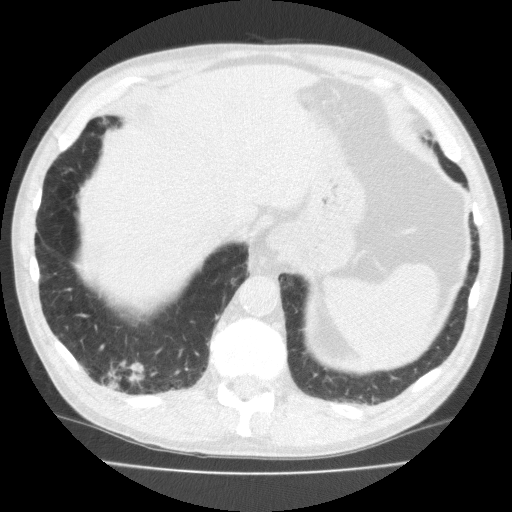
Chest CT (low-dose screening protocol), one axial image; second annual screen; lung window (W 1500 / L -600 HU); 2 mm slice thickness. Male participant, aged 70 years at enrolment. Current smoker at enrolment.
Expert reader's lesion annotation, bounding box (x1, y1, x2, y2) in pixels: (88, 349, 160, 399). Reader record for this screening exam (exam-level; its link to the box is not recorded): non-calcified nodule or mass ≥4 mm, right lower lobe, 18 × 13 mm, spiculated (stellate) margins, soft tissue attenuation, pre-existing on the prior screen: no. Later outcome: lung cancer diagnosed 64 days after this screen — squamous cell carcinoma, NOS, right lower lobe, moderately differentiated (G2), stage IA (AJCC 6th edition), 20 mm at pathology.